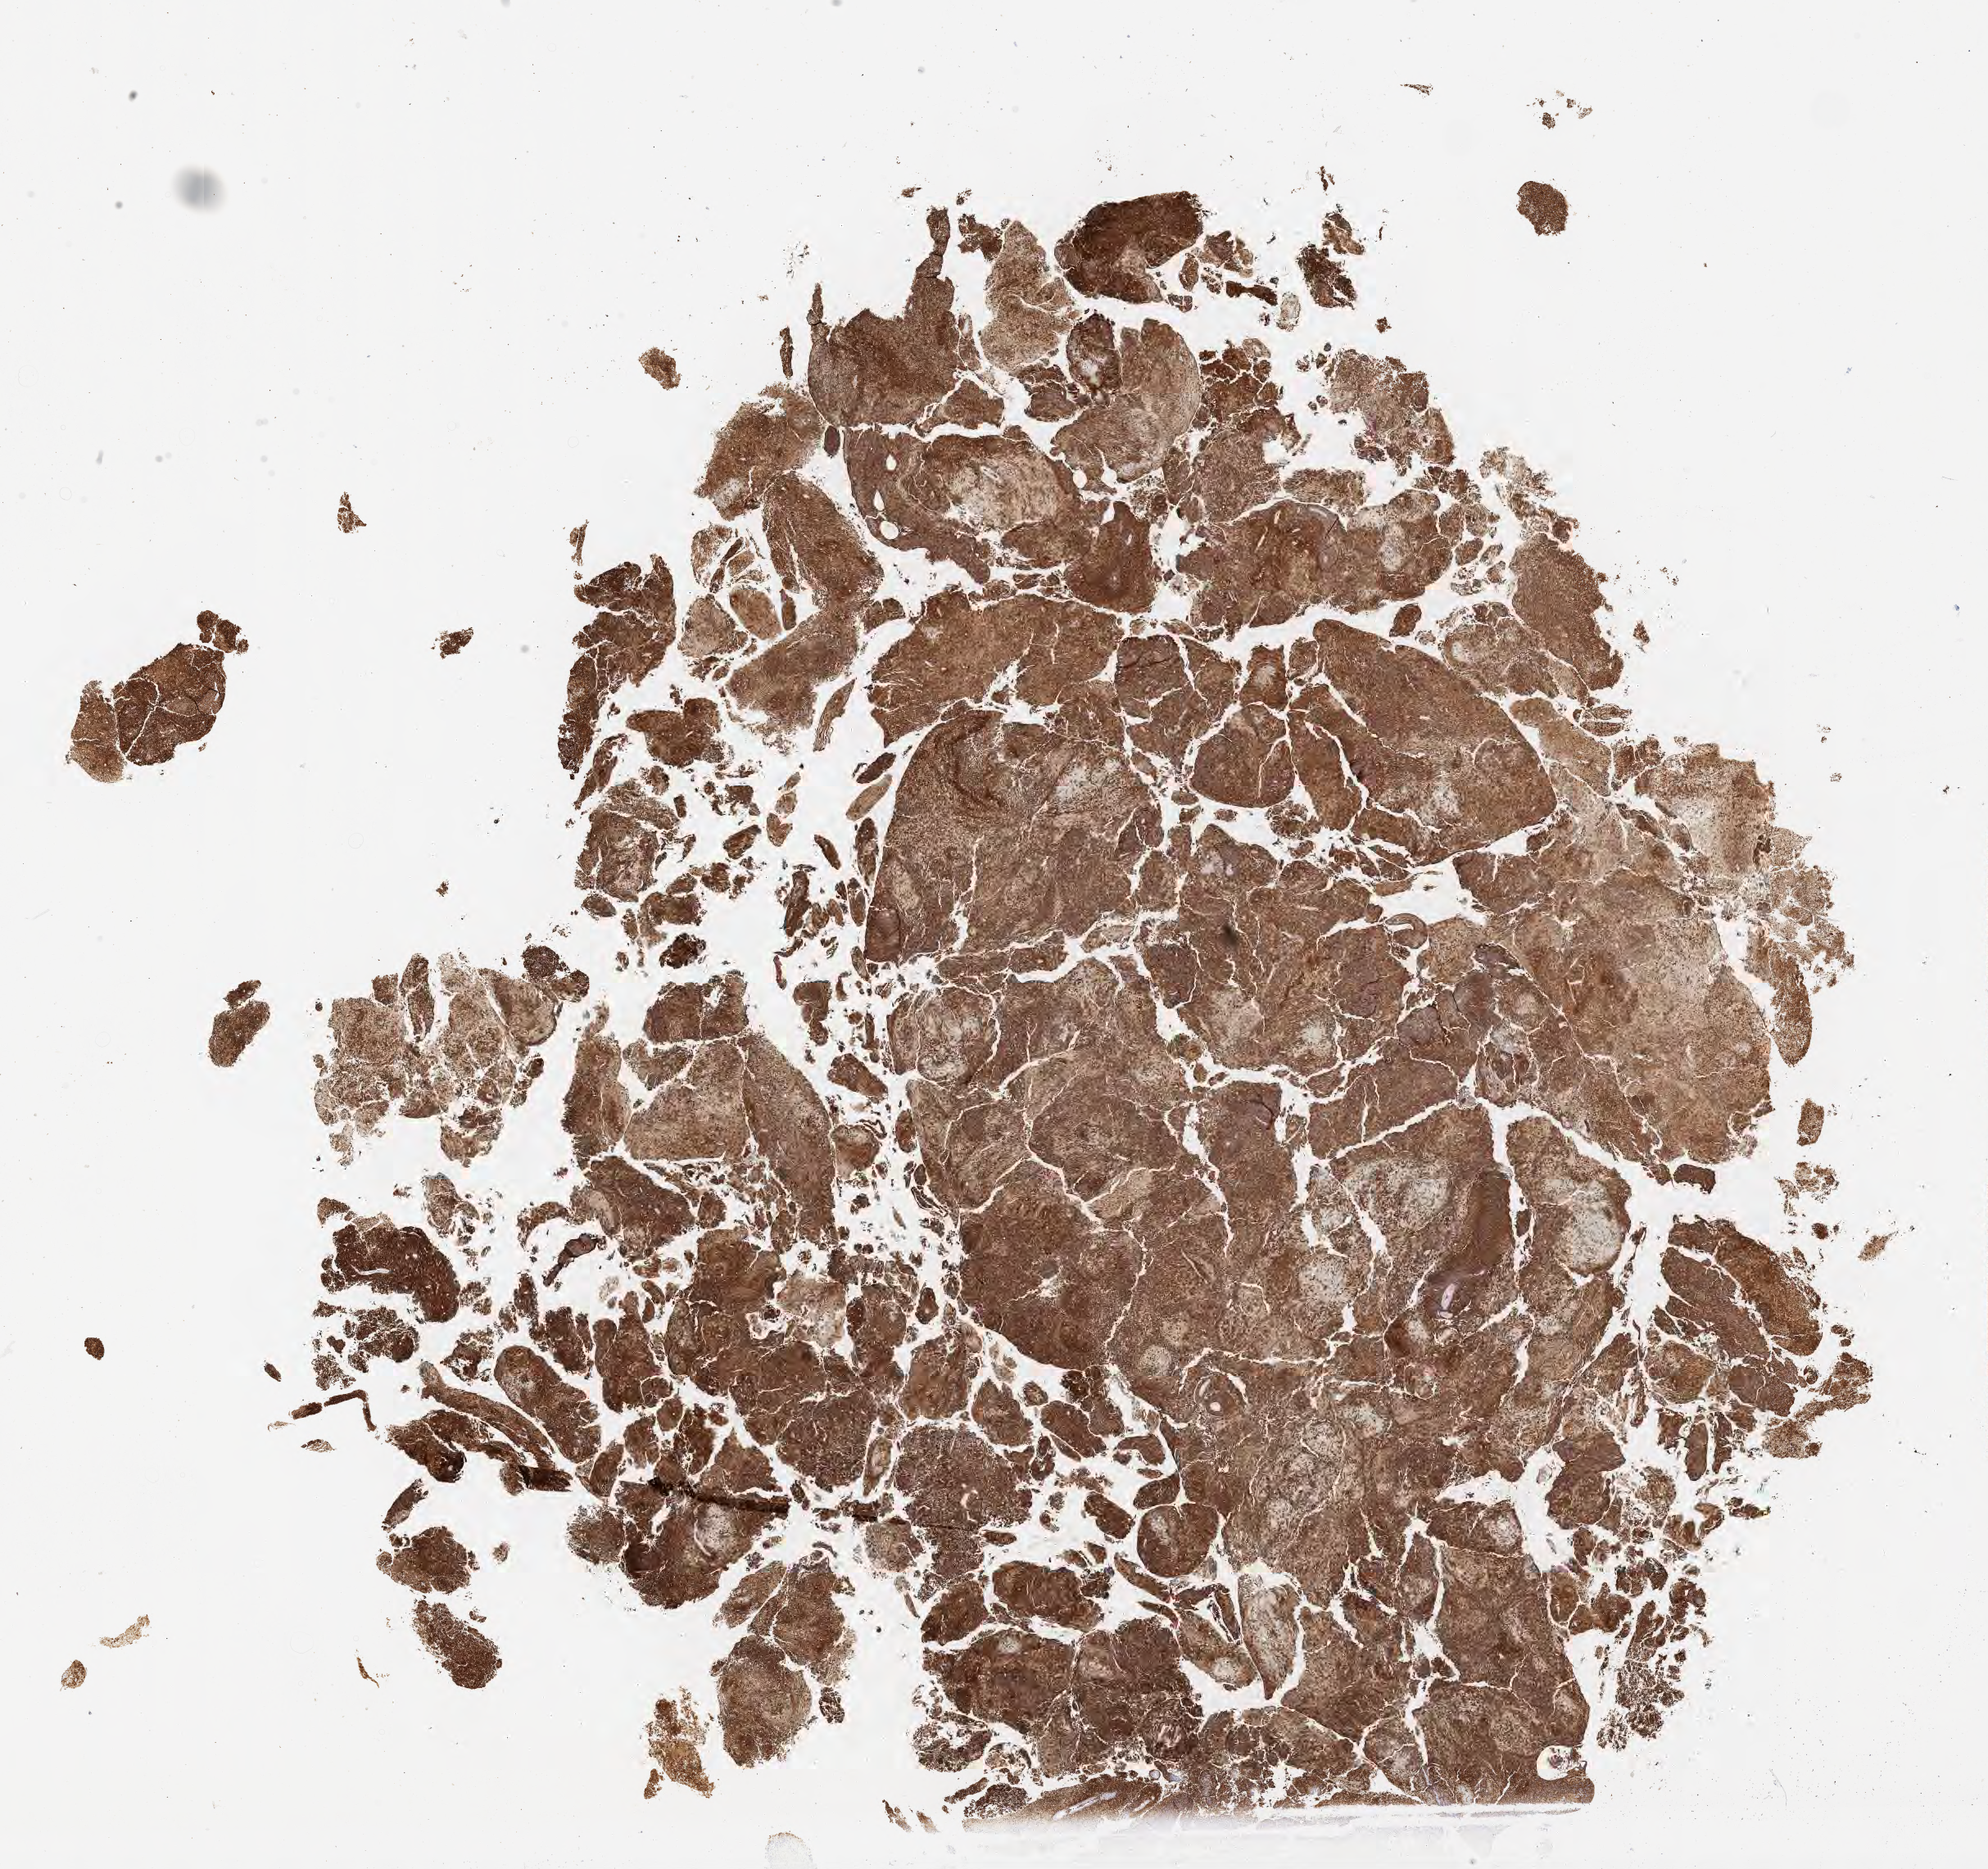
IHC for CD20, whole-slide image — low-resolution overview of the scanned area, about 19.6 x 18.5 mm. Specimen: tumor tissue. Anatomic site: brain. Patient: male, 51 years old.
• diagnosis: Diffuse large B-cell lymphoma, NOS